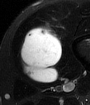
MRI of an extremity soft-tissue mass, one axial slice. Slice 21 of 65 in the series (ordered by position). T2-weighted fat-saturated. MR volume resampled by the dataset authors to the PET/CT grid (not the native acquisition matrix). 3.27 mm slice thickness. 90 × 105 image matrix, field of view 88 × 103 mm. Male patient. Case-level facts recorded for this patient, not image findings: histological type: mixoid liposarcoma; grade: low; site of the primary tumour: left thigh.
Outlined on this slice (expert contour drawn on MRI and transferred to this co-registered scan by the dataset authors):
- gross tumour volume (mass): bounding box (x1, y1, x2, y2) in pixels: (20, 25, 62, 83)